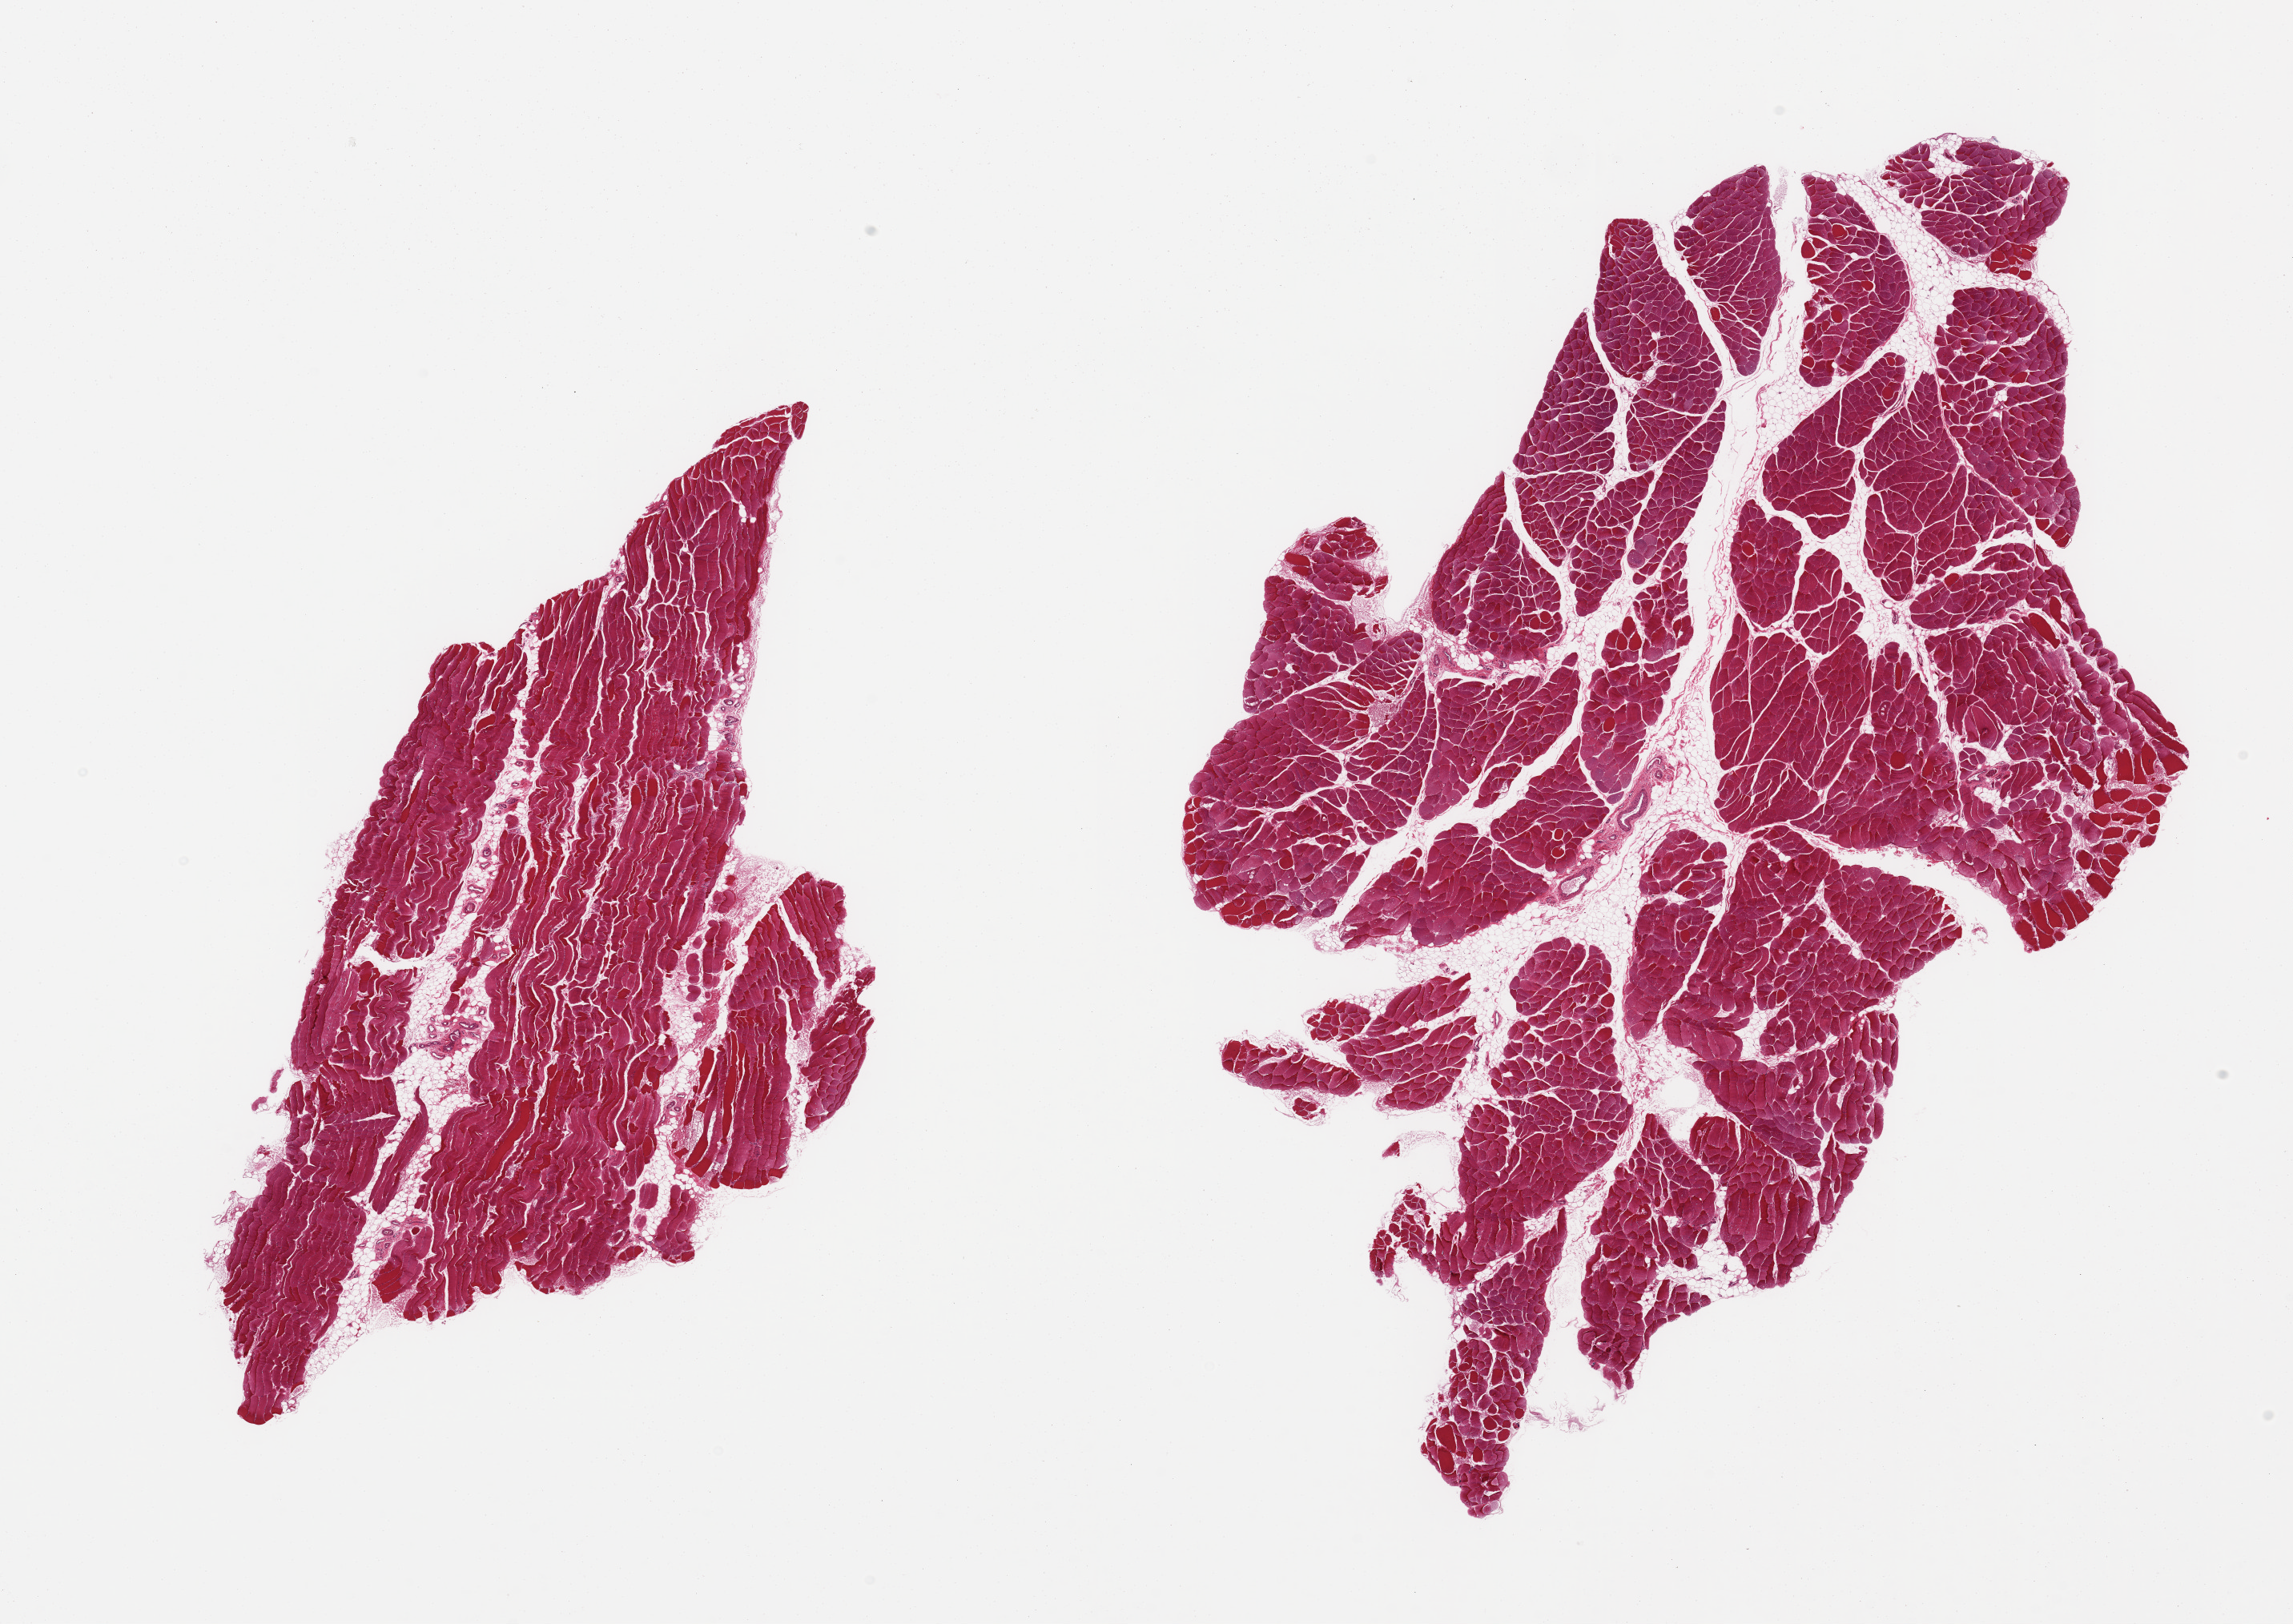
Digitized hematoxylin and eosin (H&E)-stained section — low-resolution overview of the scanned area, about 22.6 x 16.0 mm, PAXgene-fixed, paraffin-embedded tissue, sampled site (target tissue): skeletal muscle, donor tissue sample. Donor sex: male.
Pathologist's review note for this sample: 2 pieces; <5% internal fat; slight atrophy.